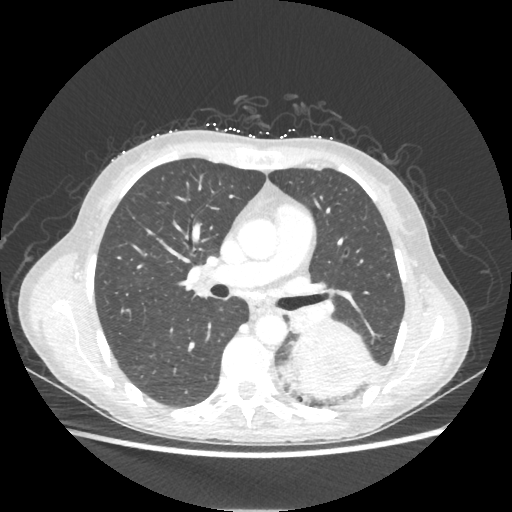
Chest CT, one axial slice. Position 123 of 221 along the scan axis. 80 kVp. Lung window (W 1500 / L -600 HU). 512 × 512 image matrix. Patient: female, 53 years. From the clinical record (not read from this slice): clinical TNM (as recorded): T3 N0 M0.
Structures marked on this image (rectangle marked by the reading radiologist):
- lung tumour (recorded histology: adenocarcinoma): box from (x=285, y=319) to (x=371, y=398) px